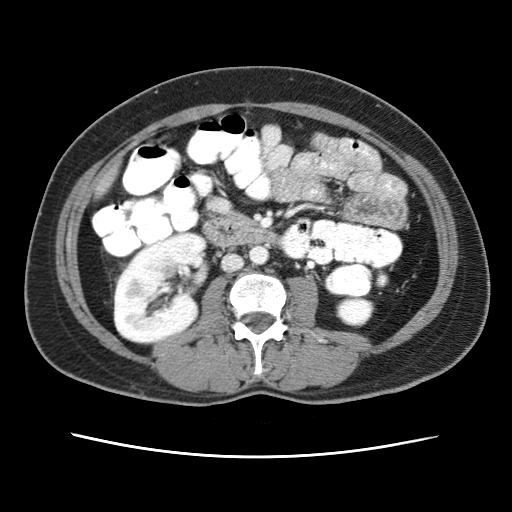
Contrast-enhanced abdominal CT (liver protocol), one axial slice. Position 2 of 79 along the scan axis. Reconstruction kernel STANDARD. Soft-tissue window (W 400 / L 40 HU). 512 × 512 image matrix, field of view 340 × 340 mm. From the clinical record (not read from this slice): diagnosis: hepatocellular carcinoma (patient treated with transarterial chemoembolisation; whether this scan precedes or follows treatment is not stated here); TNM stage (as recorded): Stage-I; Child-Pugh class: A; tumour differentiation: moderately differentiated.
Annotated regions visible in this slice (semi-automatically segmented with operator editing):
- abdominal aorta: box from (x=249, y=246) to (x=268, y=265) px
- liver parenchyma outside the tumour (the mass and vessels are separate outlines, so this box may not span the whole liver): (x=110, y=165)–(x=117, y=173)